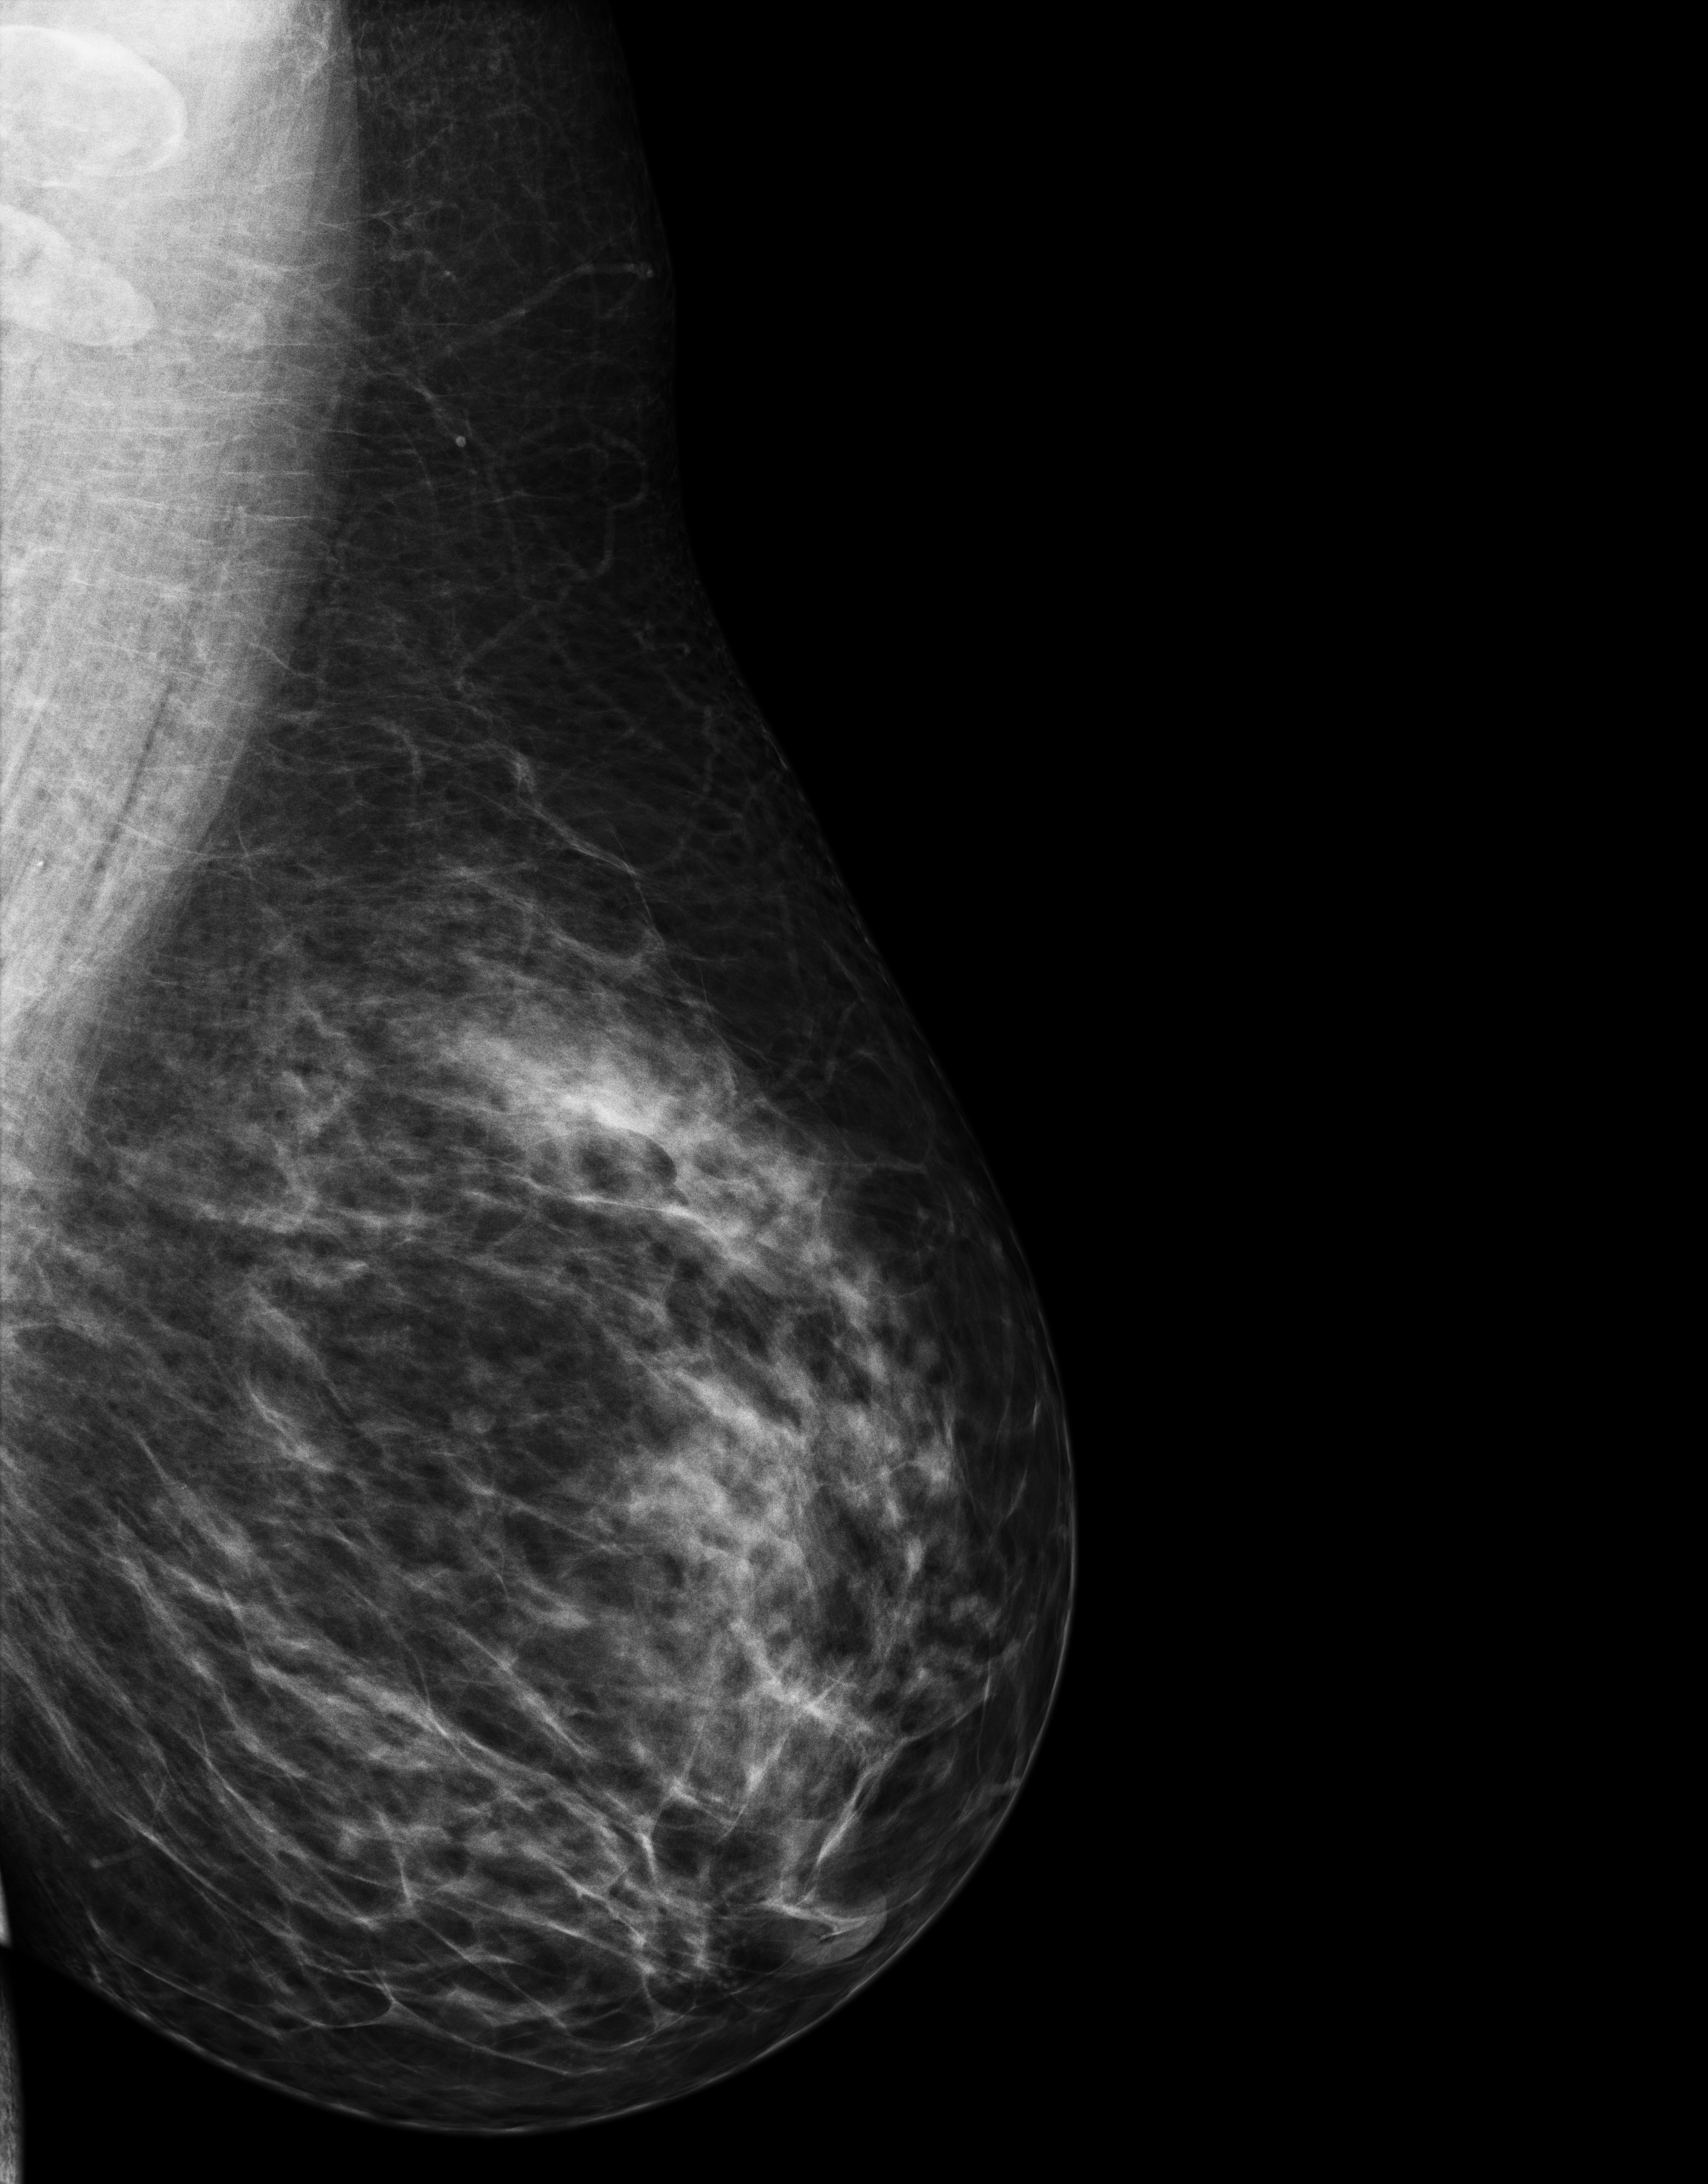
Annual screening mammography examination. Female patient, age 42 years.
Image type: full-field digital mammogram. Breast: left. Projection: mediolateral oblique (MLO) view. BI-RADS breast density category at the screening exam (both breasts, scale 1–4): 3. Final BI-RADS assessment for this screening round (tomosynthesis exam, both breasts): category 1. Recall: no recall after this screen.